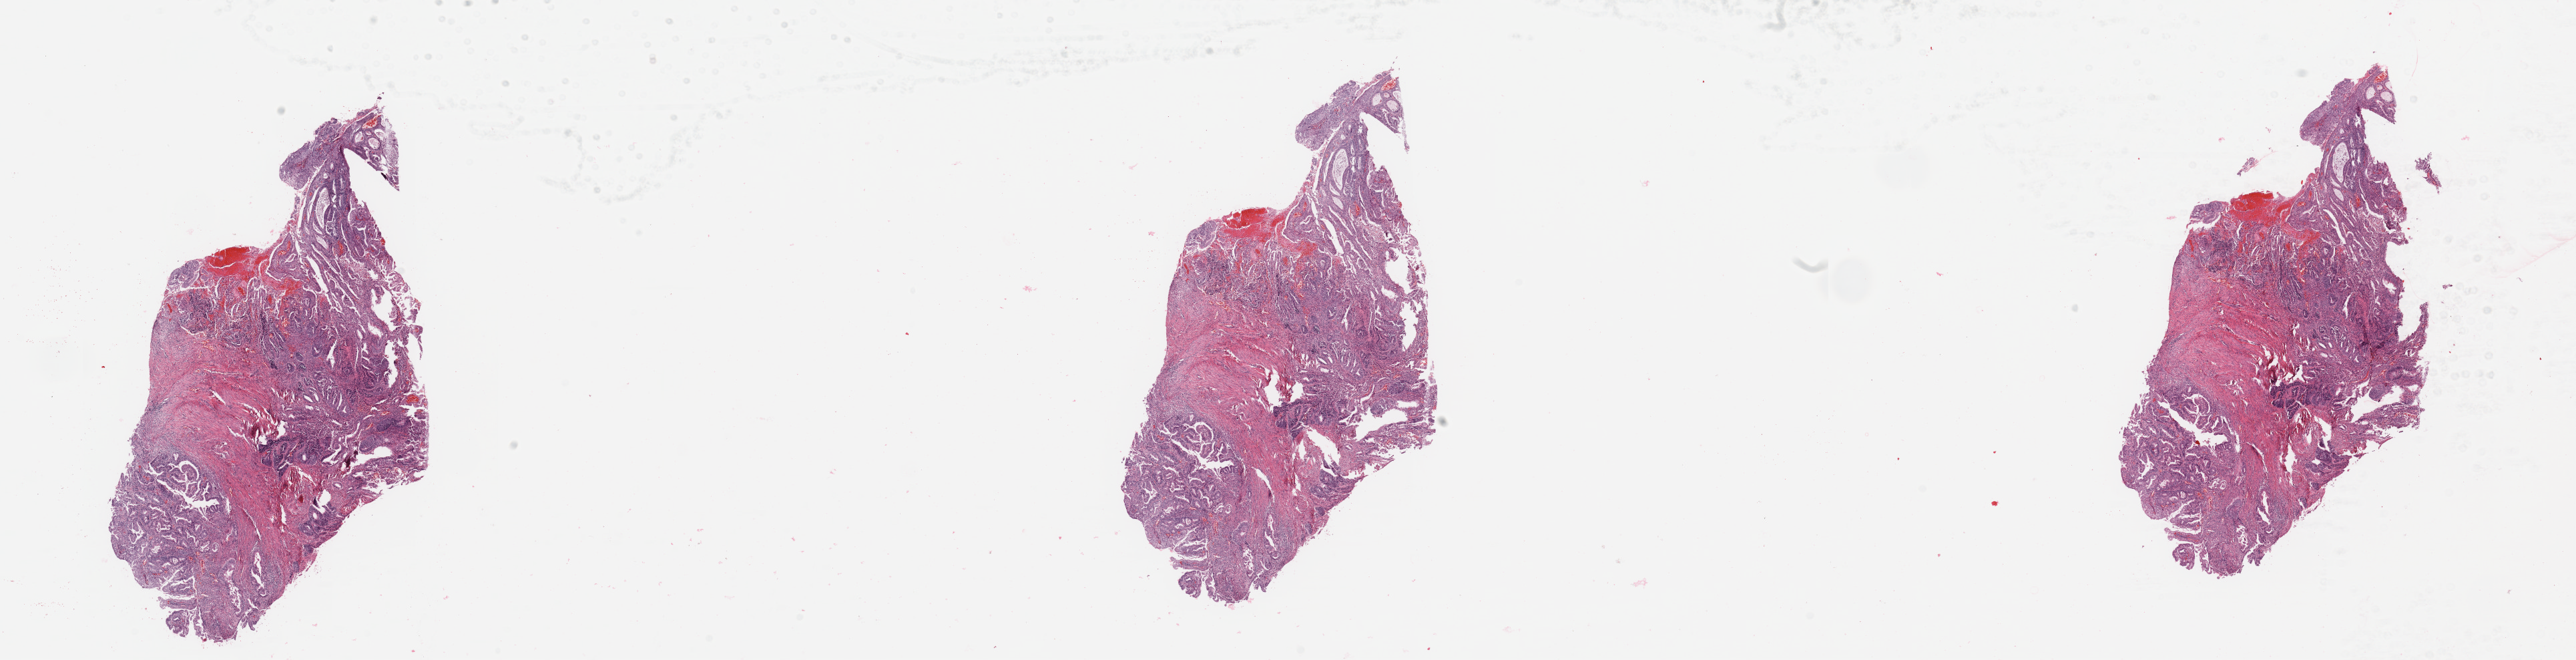
Digitized H&E tissue section (whole slide), low-resolution overview of the scanned area, about 30.5 x 7.8 mm (acquisition: 20x scan). Tumour tissue sample, uterus. Patient: female, age 74 years. Histologic grade: G2 (moderately differentiated).
Histologic diagnosis: Endometrioid adenocarcinoma, NOS. AJCC pathologic stage: IIIC1.